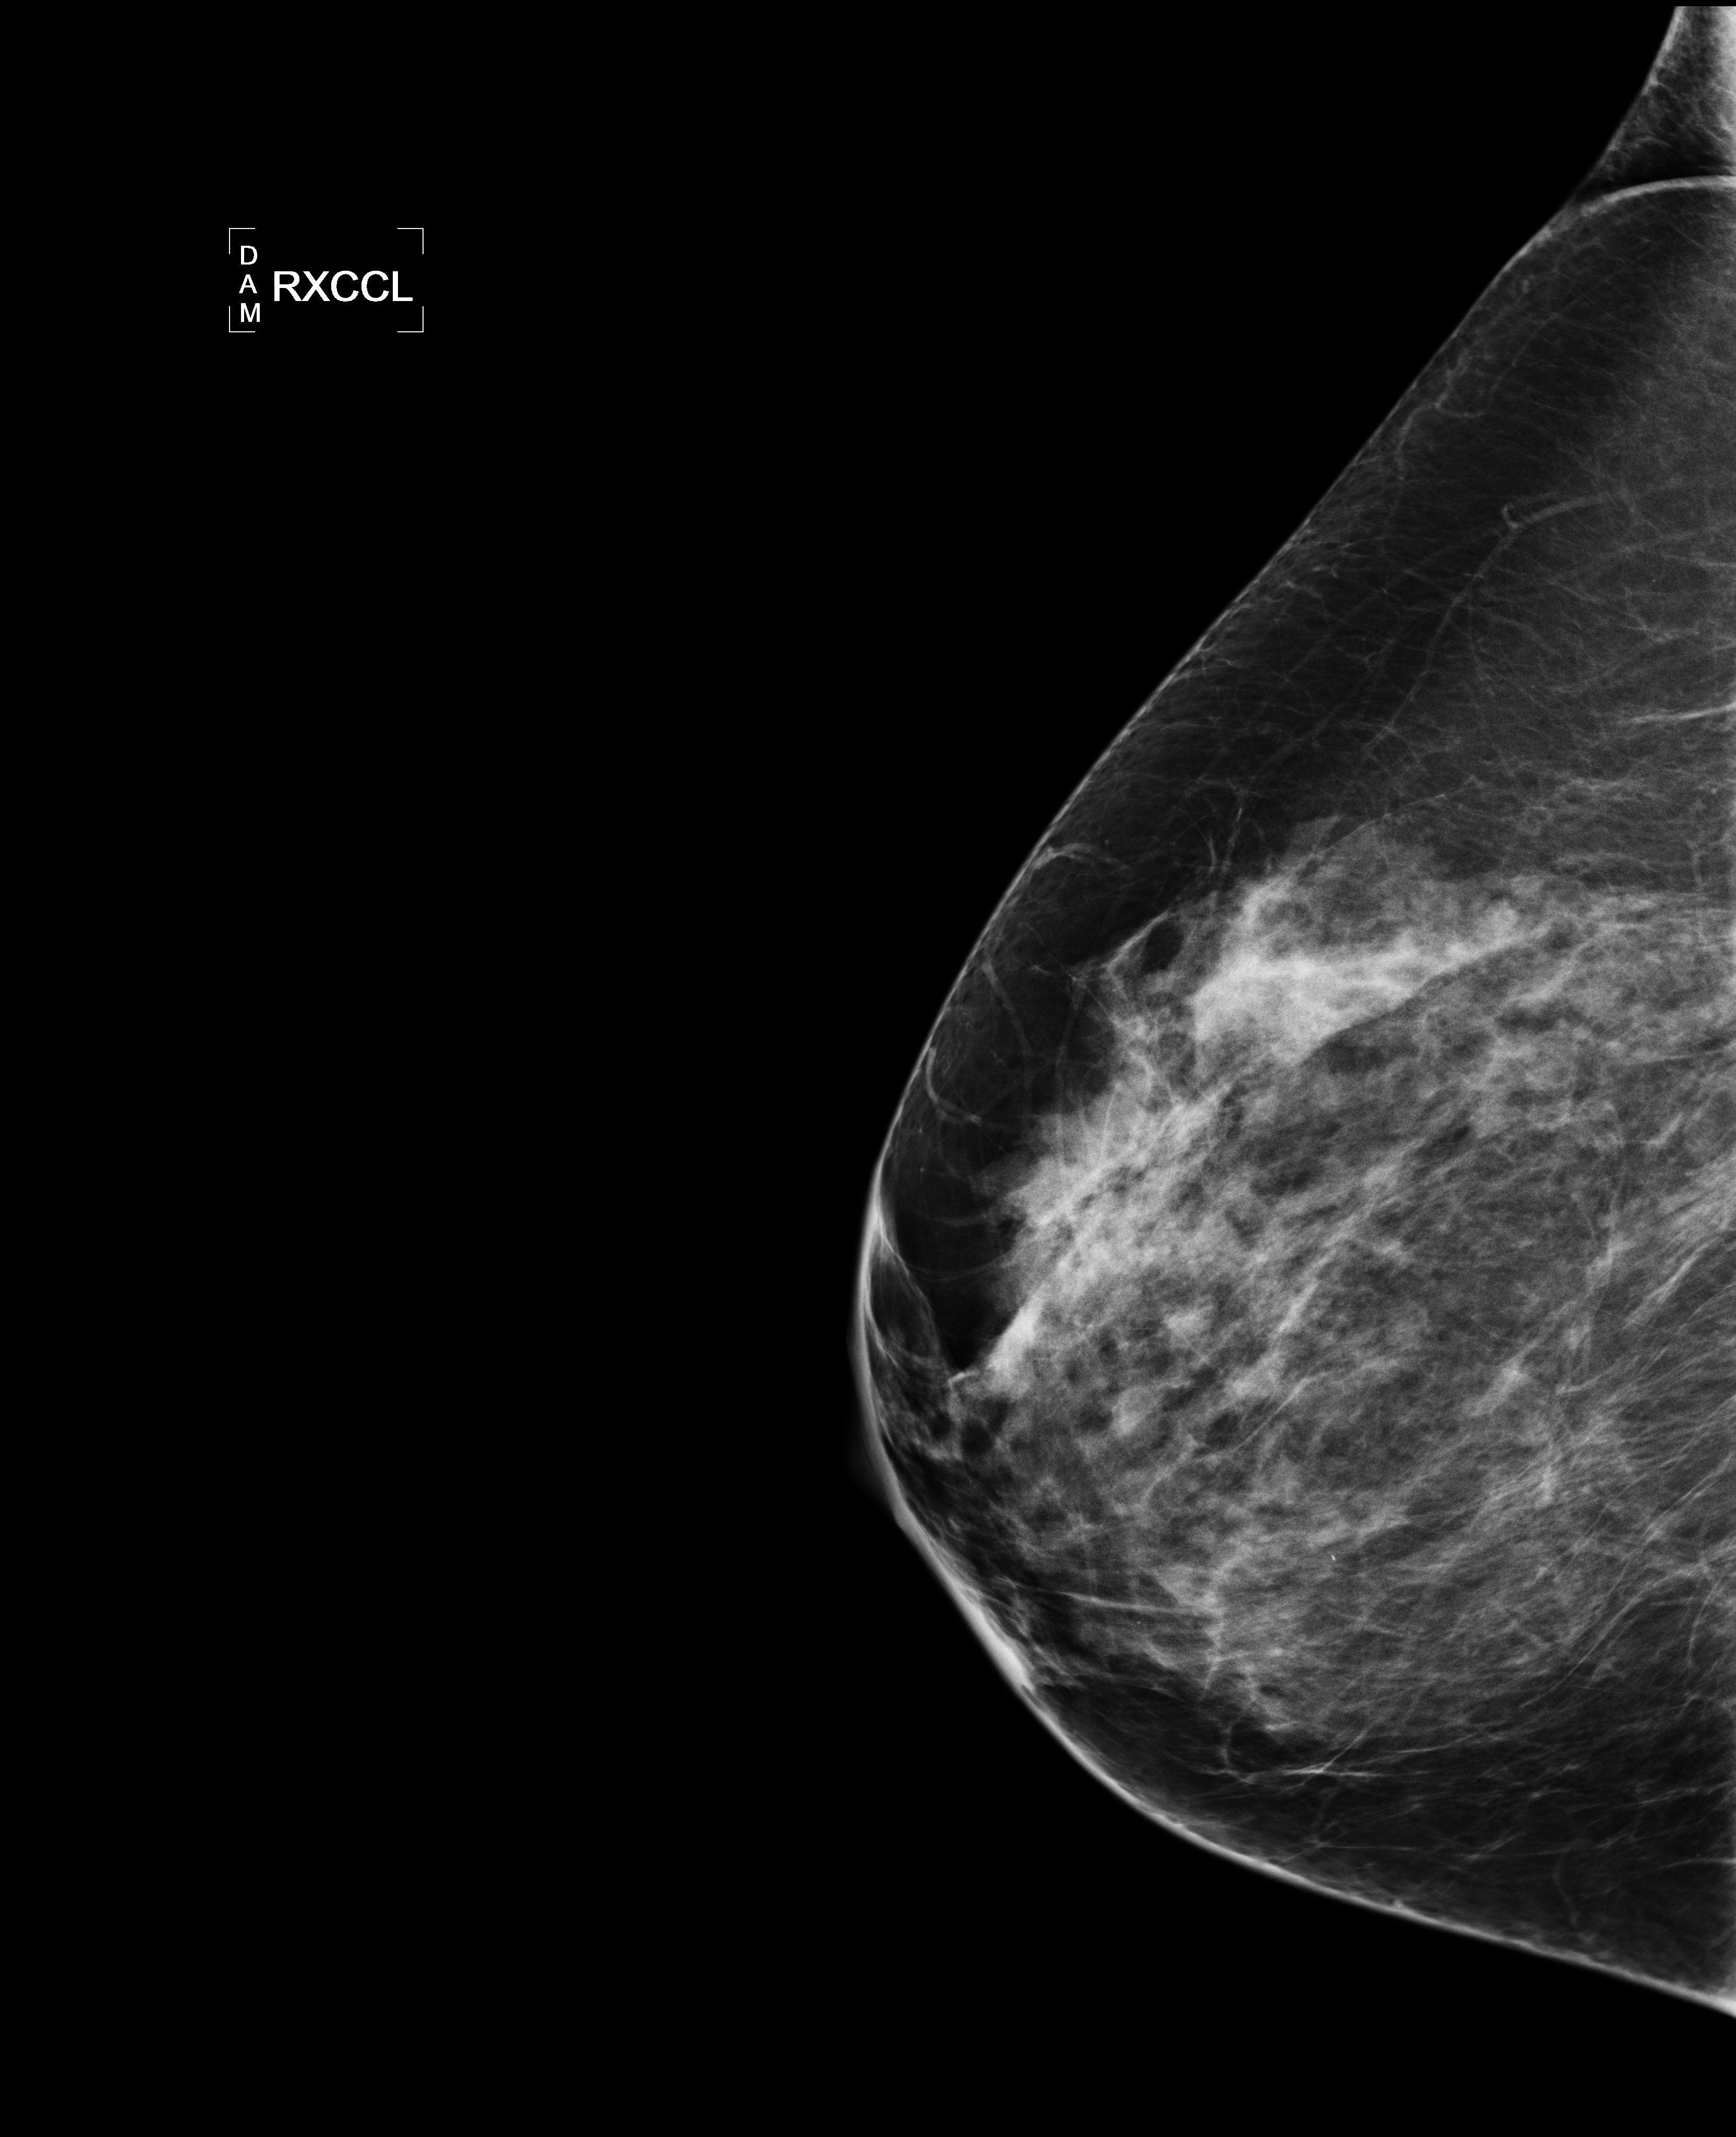
Mammogram, right breast, XCCL view; patient in her 50s.
Patient-level pathology facts (clinical record, not image findings): pathology diagnosis: Invasive ductal CA (left breast); receptor status (as recorded): ER pos, PR pos (weak), HER2 neg; pathology report notes: re-bx [date] was scar tissue from RT rx.